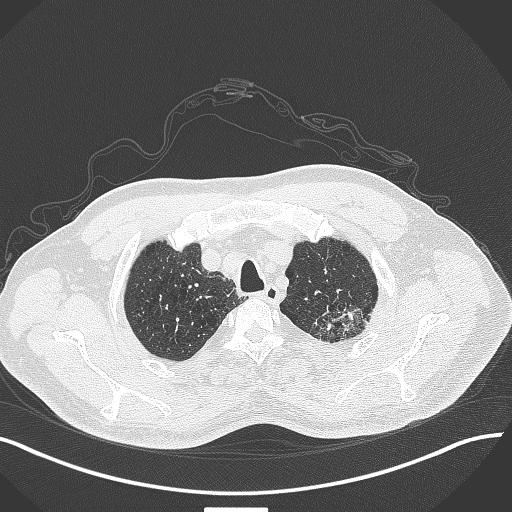
Chest CT, one axial slice. Position 364 of 429 along the scan axis. Lung window (W 1500 / L -600 HU). 512 × 512 image matrix, field of view 400 × 400 mm. Patient: male, 55 years. Case-level facts recorded for this patient, not image findings: clinical TNM (as recorded): T3 N0 M1c.
Annotated regions visible in this slice (rectangle marked by the reading radiologist):
- lung tumour (recorded histology: adenocarcinoma): bounding box <305,296,371,344> (left, top, right, bottom; pixels)